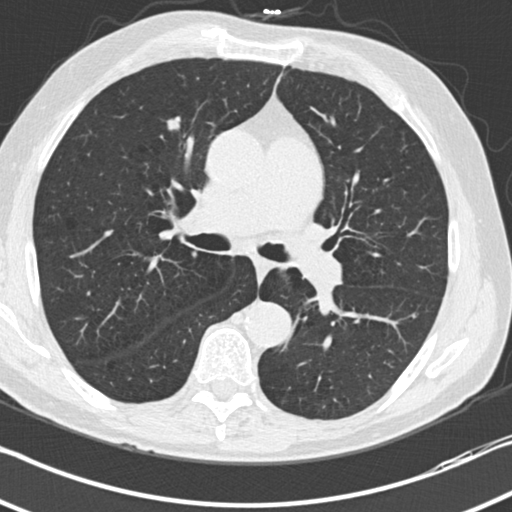
Low-dose screening chest CT, one axial slice; 120 kVp; lung window (W 1500 / L -600 HU); 512 × 512 image matrix.
Outlined on this slice (manually delineated by an expert):
- lesion 1 (tumor, upper lobe of right lung): bounding box (x1, y1, x2, y2) in pixels: (168, 117, 180, 130)